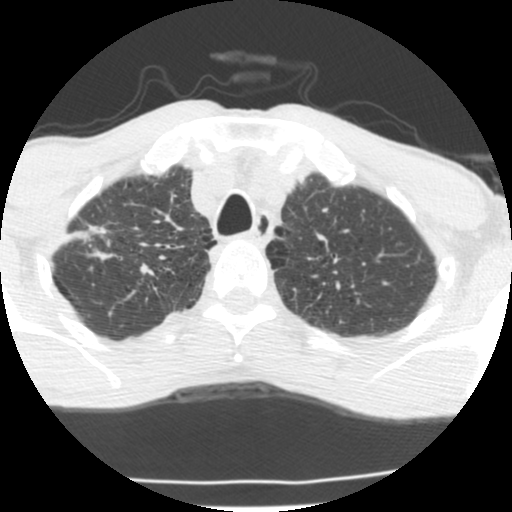
Low-dose screening chest CT, axial slice, second screening round (one year after baseline), lung window (W 1500 / L -600 HU), 2.5 mm slice thickness, standard (soft-tissue) reconstruction kernel (STANDARD), 512 × 512 image matrix, field of view 283 × 283 mm. Male, age 62 years at enrolment. Current smoker at enrolment.
Expert-annotated lung lesion, bounding box (x1, y1, x2, y2) in pixels: (51, 215, 129, 270). Reader record for this screening exam (exam-level; its link to the box is not recorded): non-calcified nodule or mass ≥4 mm, right upper lobe, 23 × 11 mm, spiculated (stellate) margins, soft tissue attenuation, pre-existing on the prior screen: yes. Official screen result: positive, change unspecified: nodule(s) >= 4 mm or enlarging nodule(s), mass(es), or other non-specific abnormalities suspicious for lung cancer. Participant outcome: lung cancer diagnosed 277 days after this screen — adenocarcinoma, NOS, right upper lobe, poorly differentiated (G3), stage IIA (AJCC 6th edition), 22 mm at pathology.